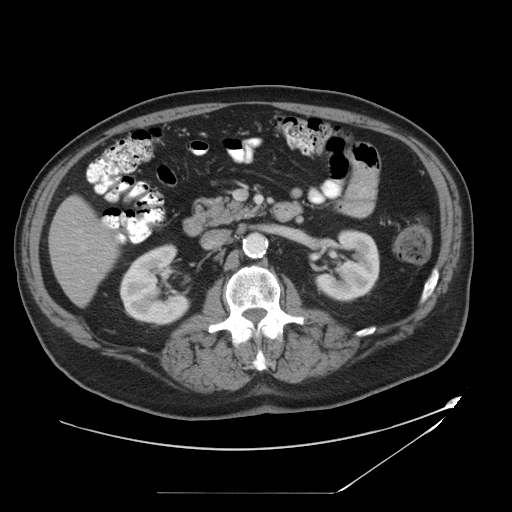
Contrast-enhanced abdominal CT, one axial slice; reconstruction kernel STANDARD; 120 kVp; intravenous contrast given; soft-tissue window (W 400 / L 40 HU); 5 mm slice thickness; 512 × 512 image matrix, field of view 461 × 461 mm. Male patient, age 72 years. Case-level facts recorded for this patient, not image findings: diagnosis: colorectal cancer liver metastases, imaged before liver resection; multiple liver metastases: no; largest metastasis: 2.5 cm; disease in both lobes: no.
Structures marked on this image (manually delineated by an expert):
- liver: bounding box [x1, y1, x2, y2] px = [51, 198, 117, 304]
- planned liver remnant (the part of the liver to remain after resection): [51, 198, 117, 304]